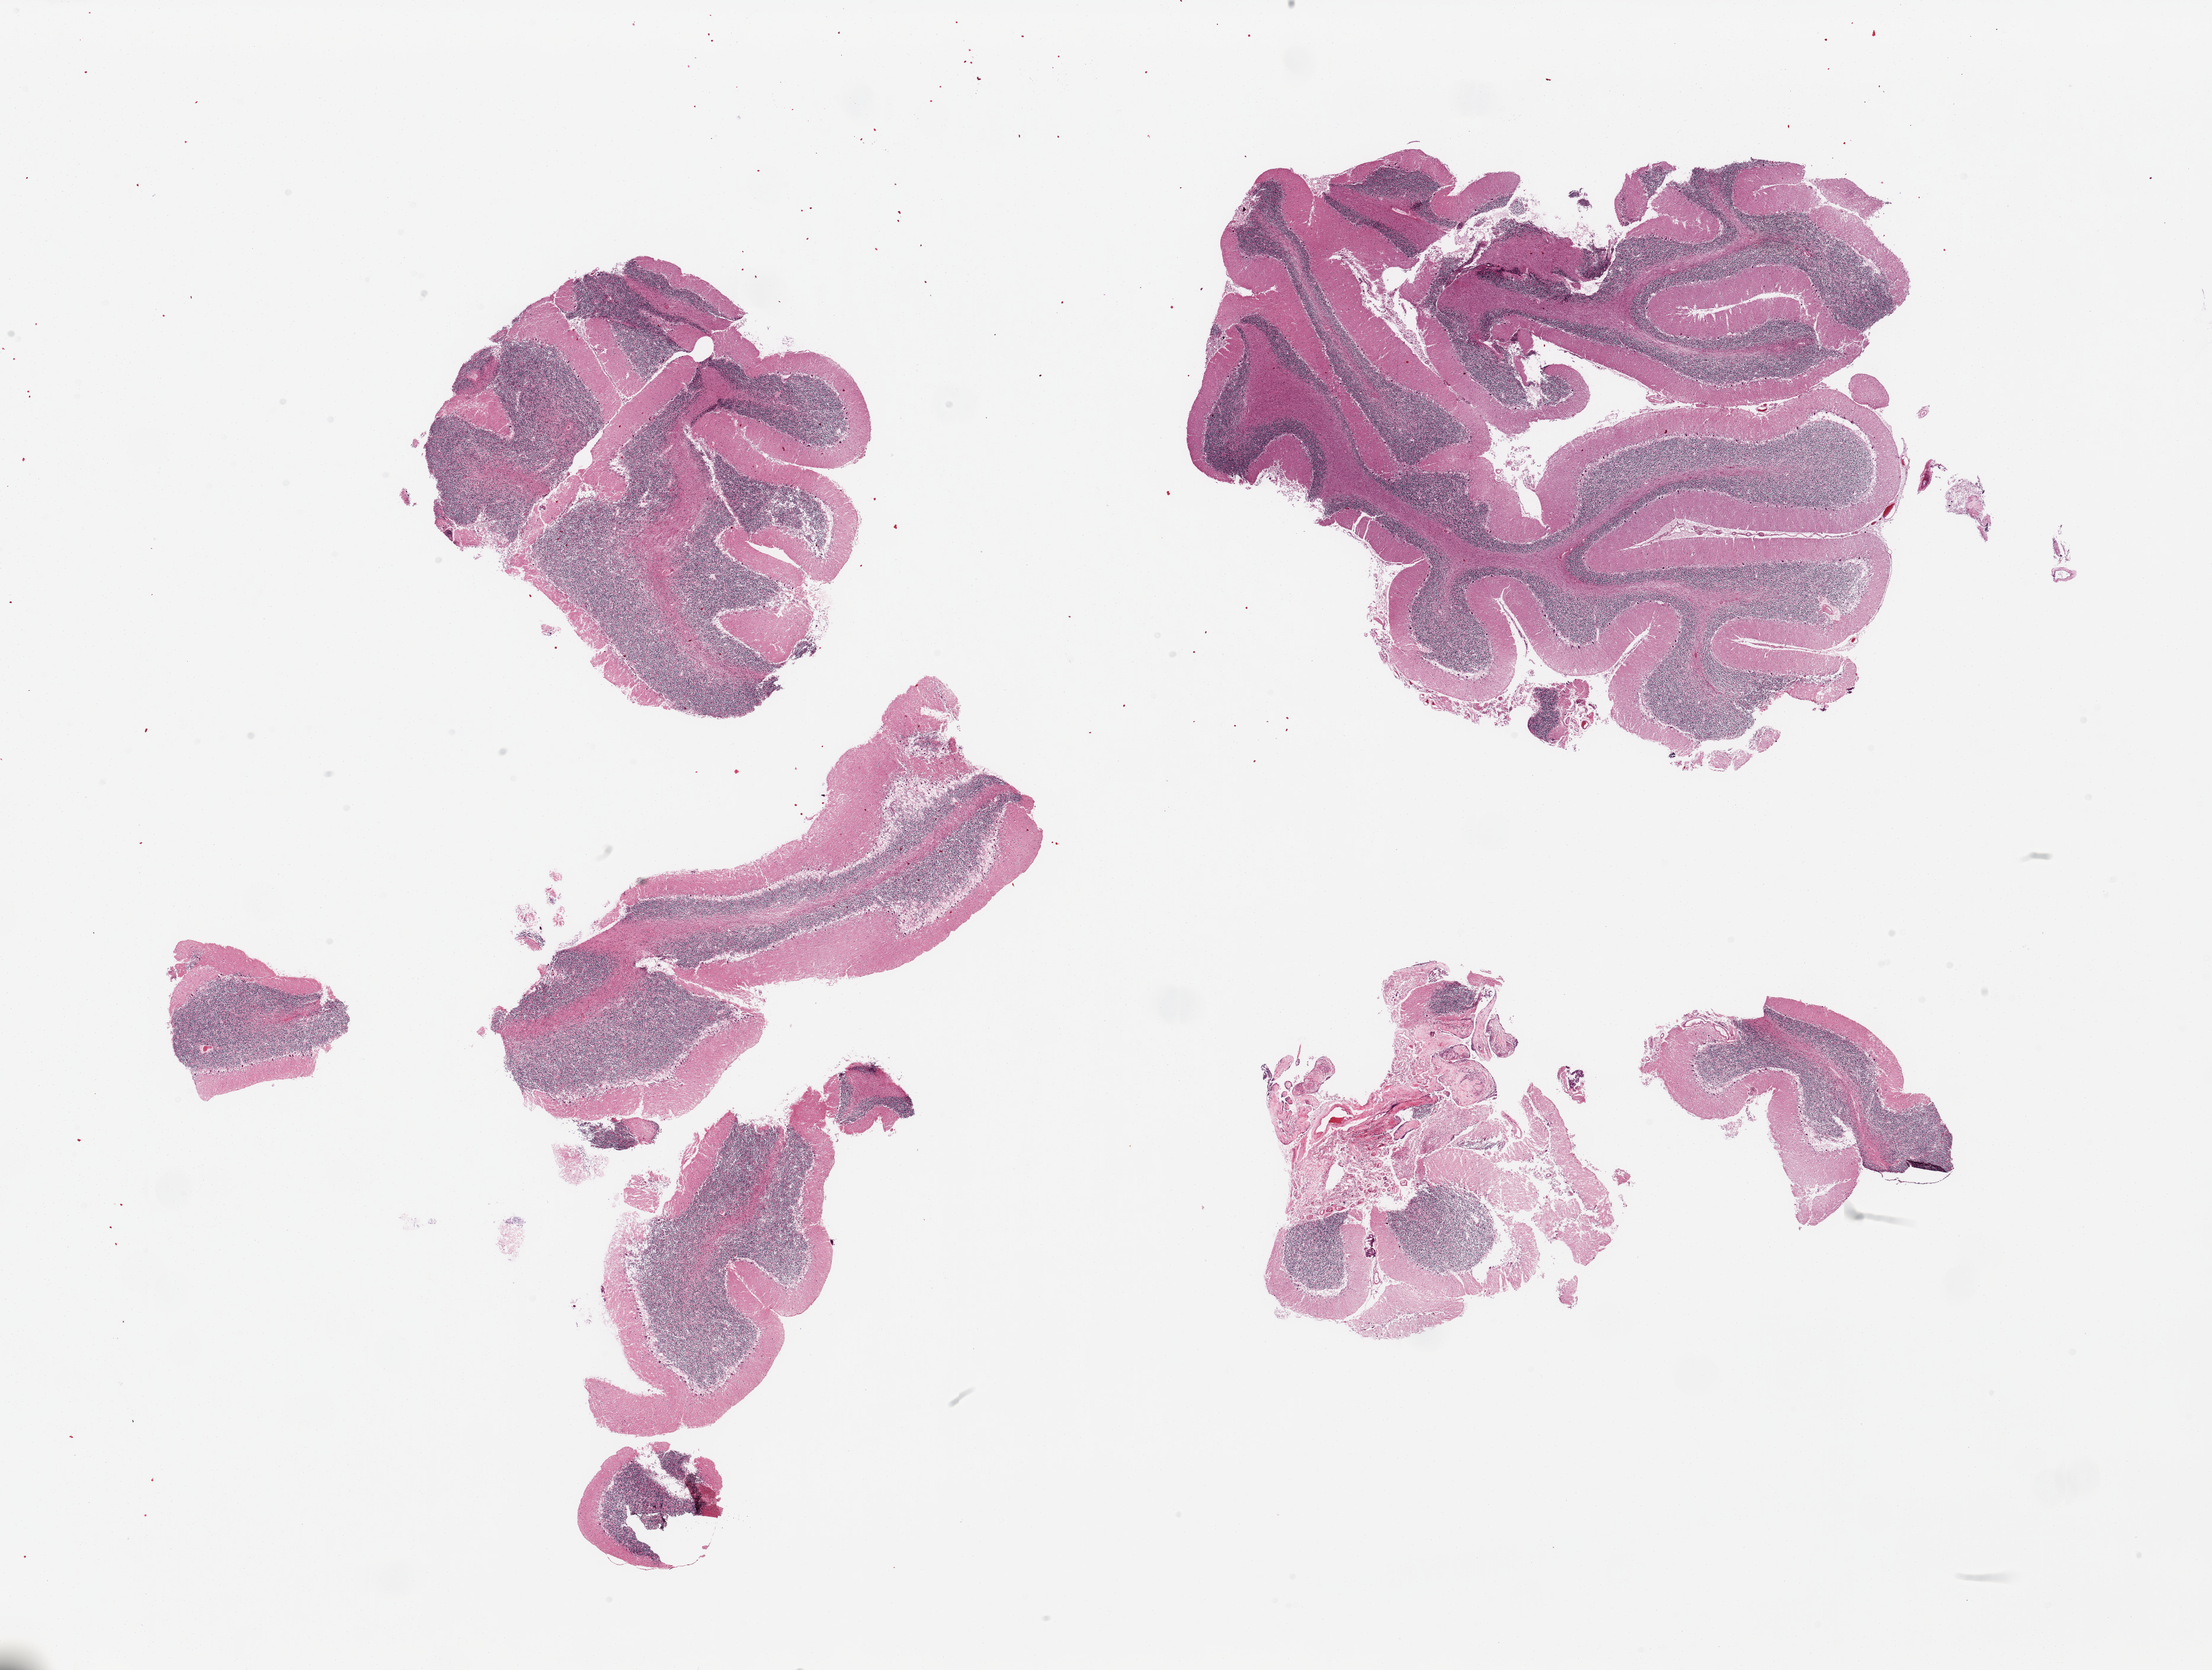
Hematoxylin and eosin (H&E) whole-slide image, low-resolution overview of the scanned area, about 29.5 x 22.3 mm; PAXgene-fixed, paraffin-embedded tissue; target tissue: cerebellum; tissue donor sample. Donor sex: female.
• review note (as recorded): 4 pieces, no abnormalities